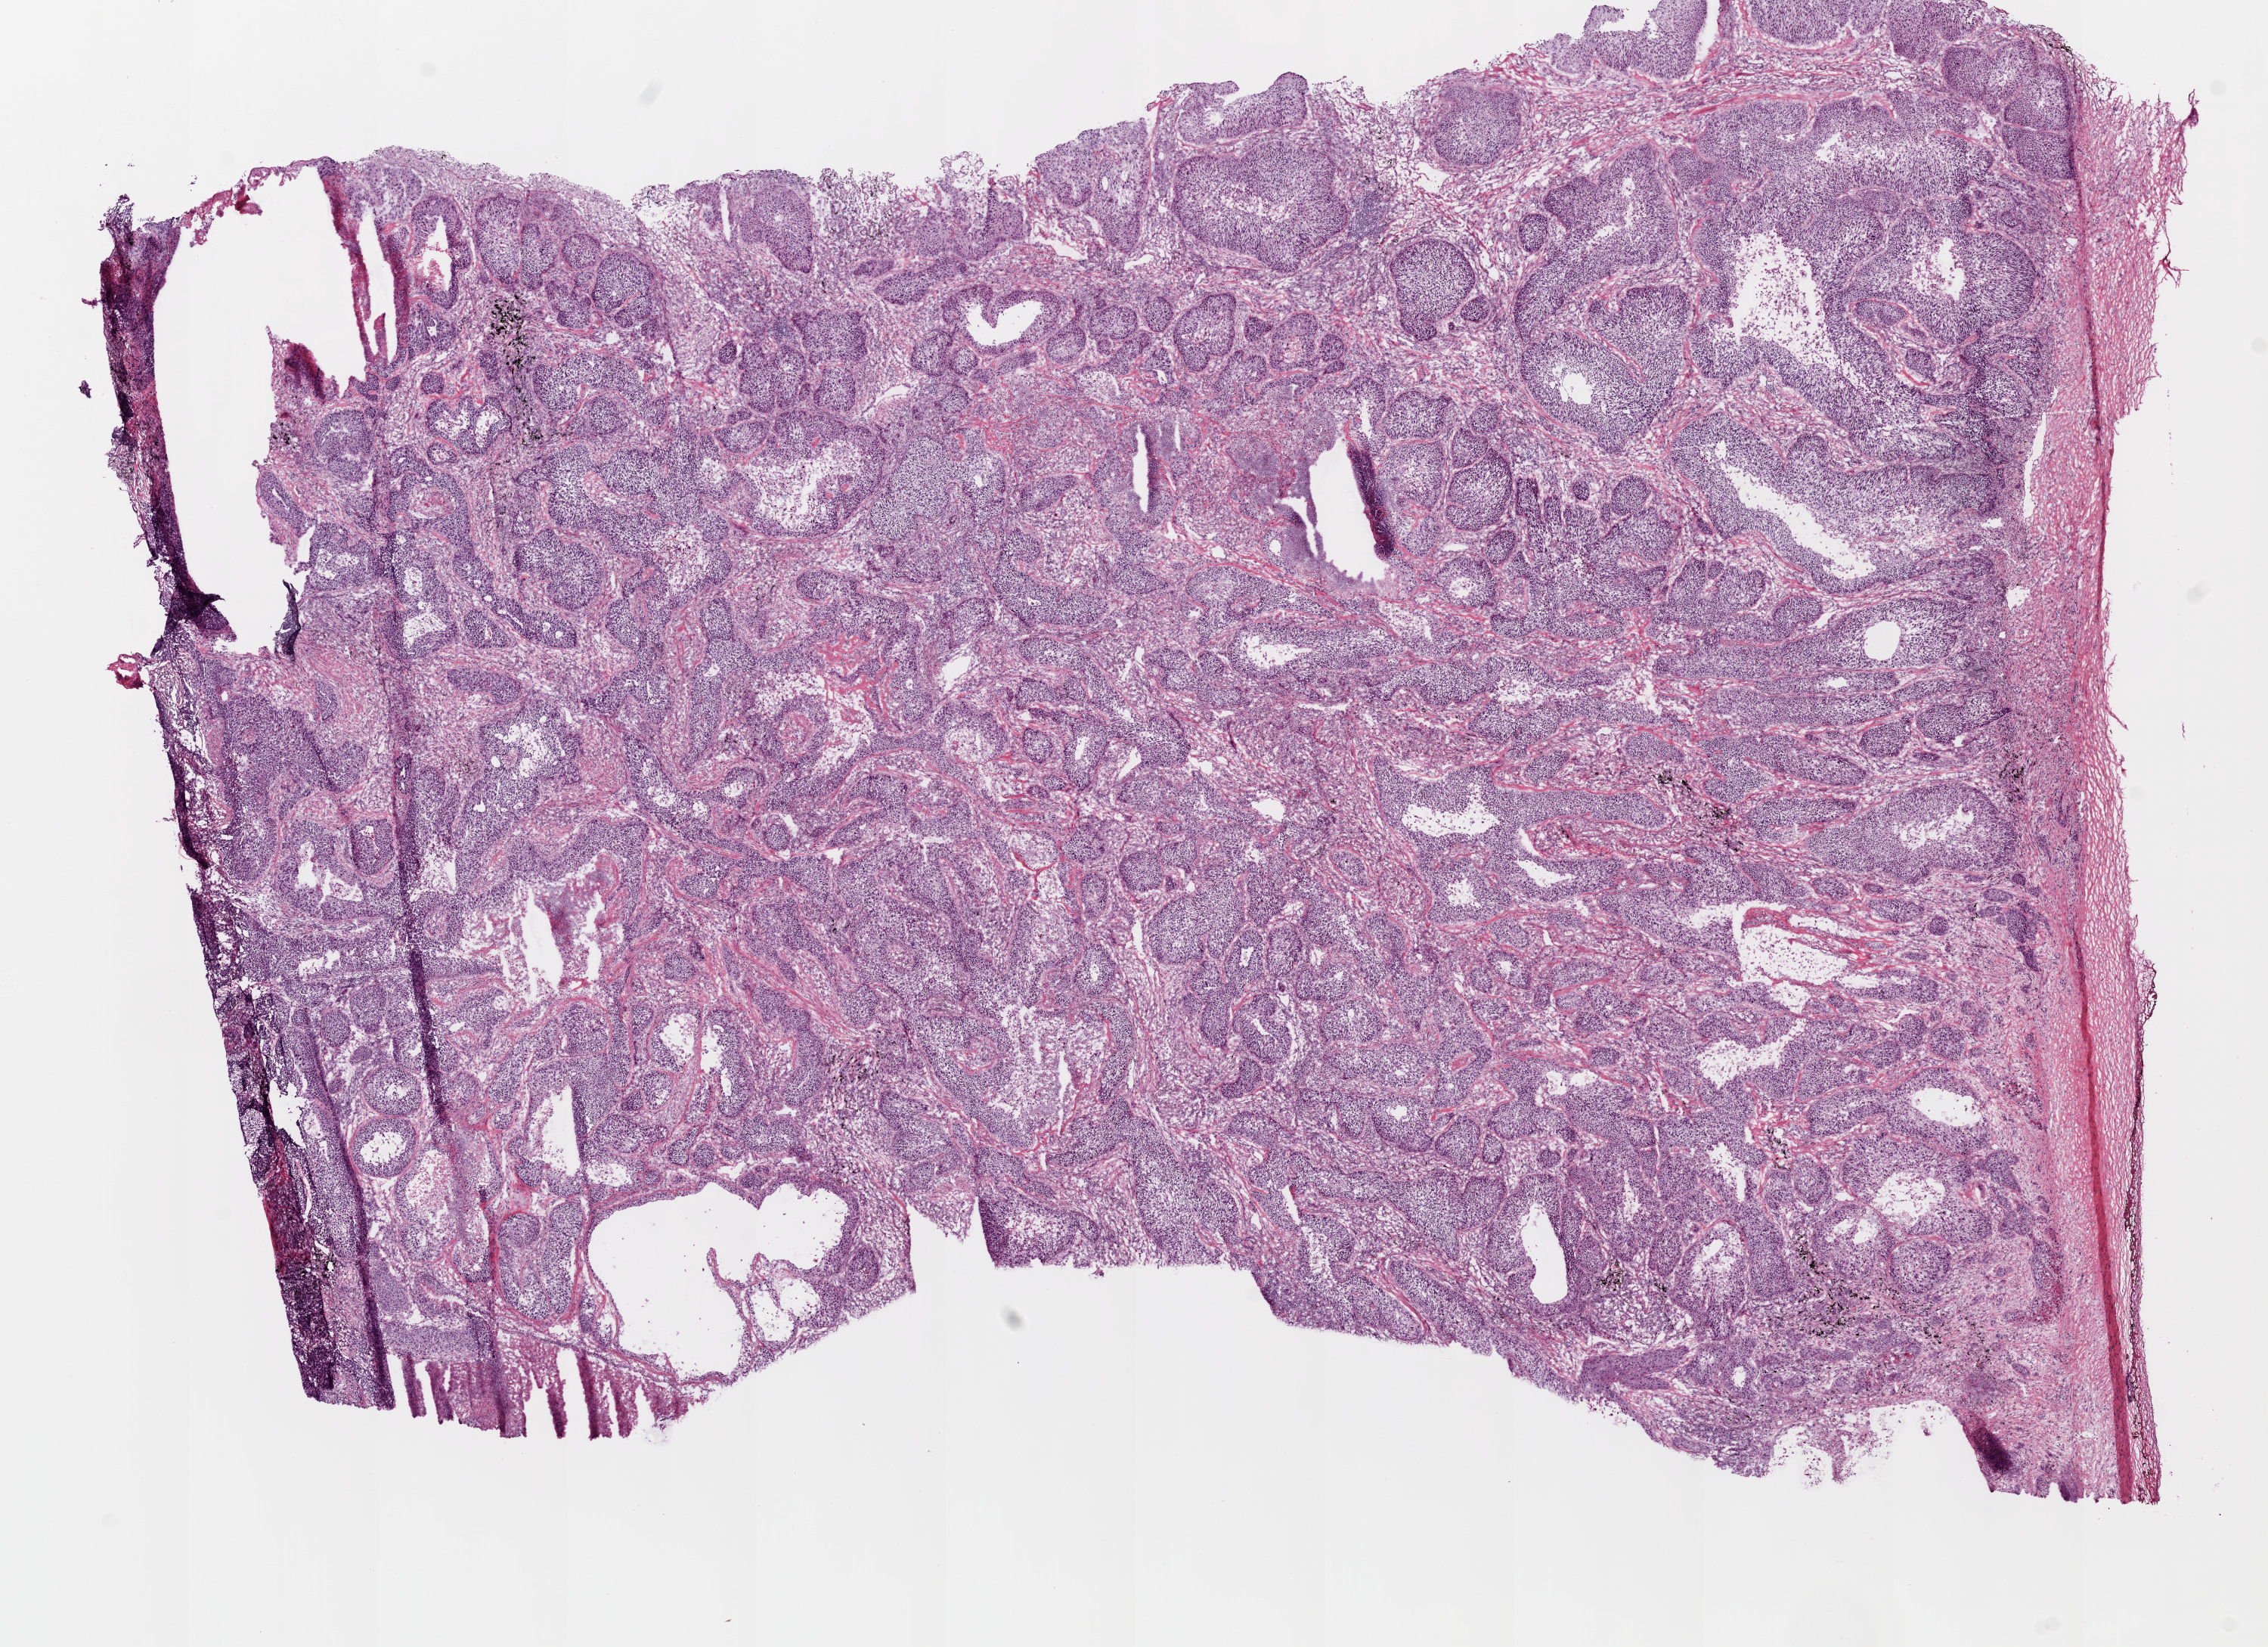
H&E whole-slide image — low-resolution overview of the scanned area, about 12.0 x 8.7 mm (slide scanned at 20x). Frozen section from the bottom of the tissue portion. Sample: primary tumour, lung. Patient: male, age at initial diagnosis 75 years. Pathologist review of this section (percent, as recorded): tumour cells 65%, tumour nuclei 75%, normal cells 0%, stromal cells 15%, necrosis 20%.
• TNM: T2a N0 M0
• AJCC pathologic stage: IB
• histologic diagnosis: Squamous cell carcinoma, NOS (lower lobe, lung)